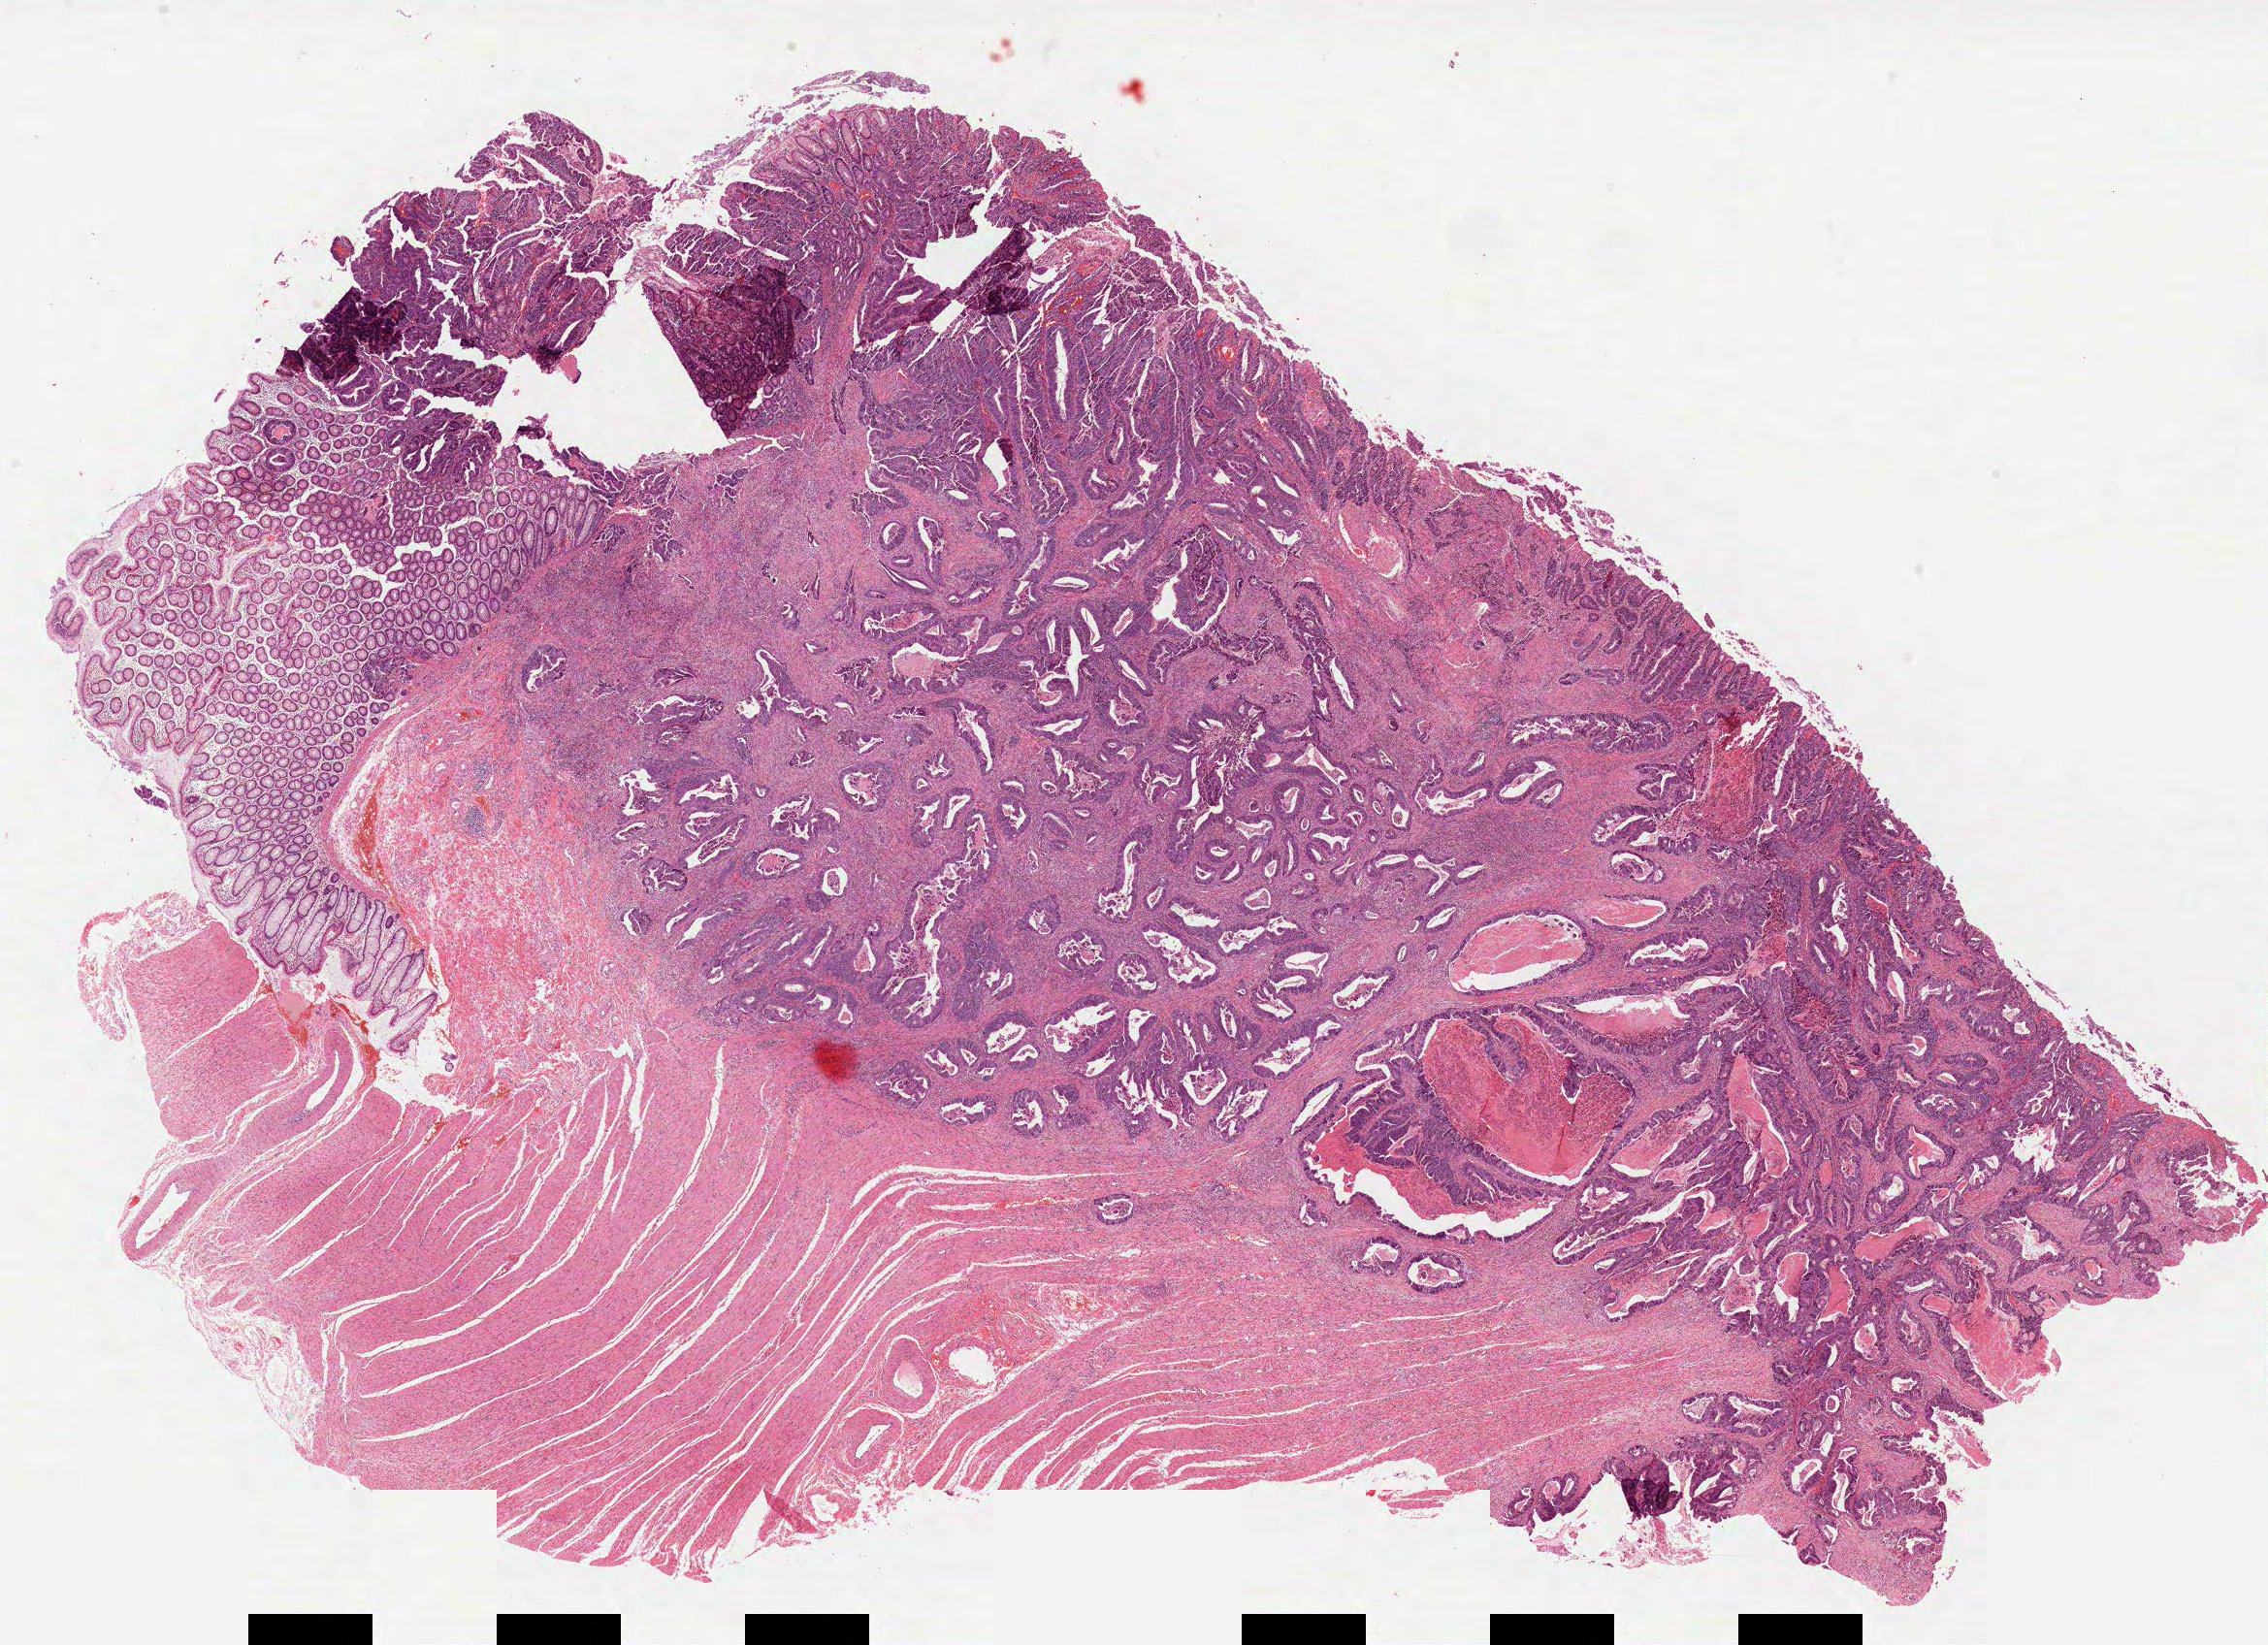
Hematoxylin and eosin (H&E) stained whole-slide image — a low-resolution overview of the entire scanned area, about 18.9 x 13.7 mm (acquisition: 40x scan), FFPE section, colon, primary tumour sample. Male patient; age at initial diagnosis 60 years.
AJCC pathologic stage: I (7th edition). Pathologic diagnosis: Adenocarcinoma, NOS. Lymph nodes positive (case pathology): 0 of 19 examined. TNM: T2 N0 M0.